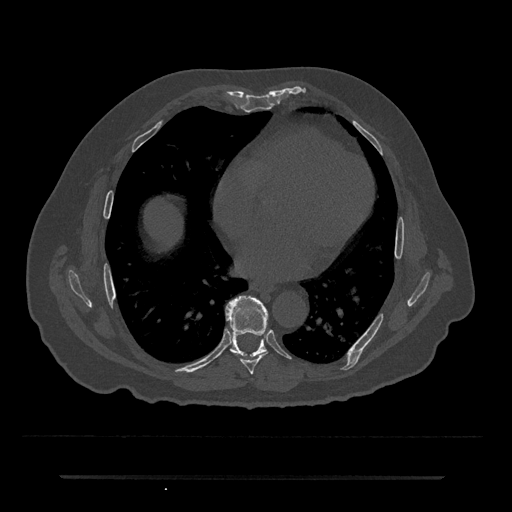
CT including the spine, one axial slice; slice 360 of 797 in the series (ordered by position); reconstruction kernel Br40s/3; bone window (W 1800 / L 400 HU); 512 × 512 image matrix. Male patient, age 69 years. From the clinical record (not read from this slice): primary cancer: prostate.
Outlined on this slice (semi-automatically segmented with operator editing):
- T7 vertebra: bounding box (x1, y1, x2, y2) in pixels: (240, 351, 268, 374)
- T8 vertebra: (226, 295, 268, 357)